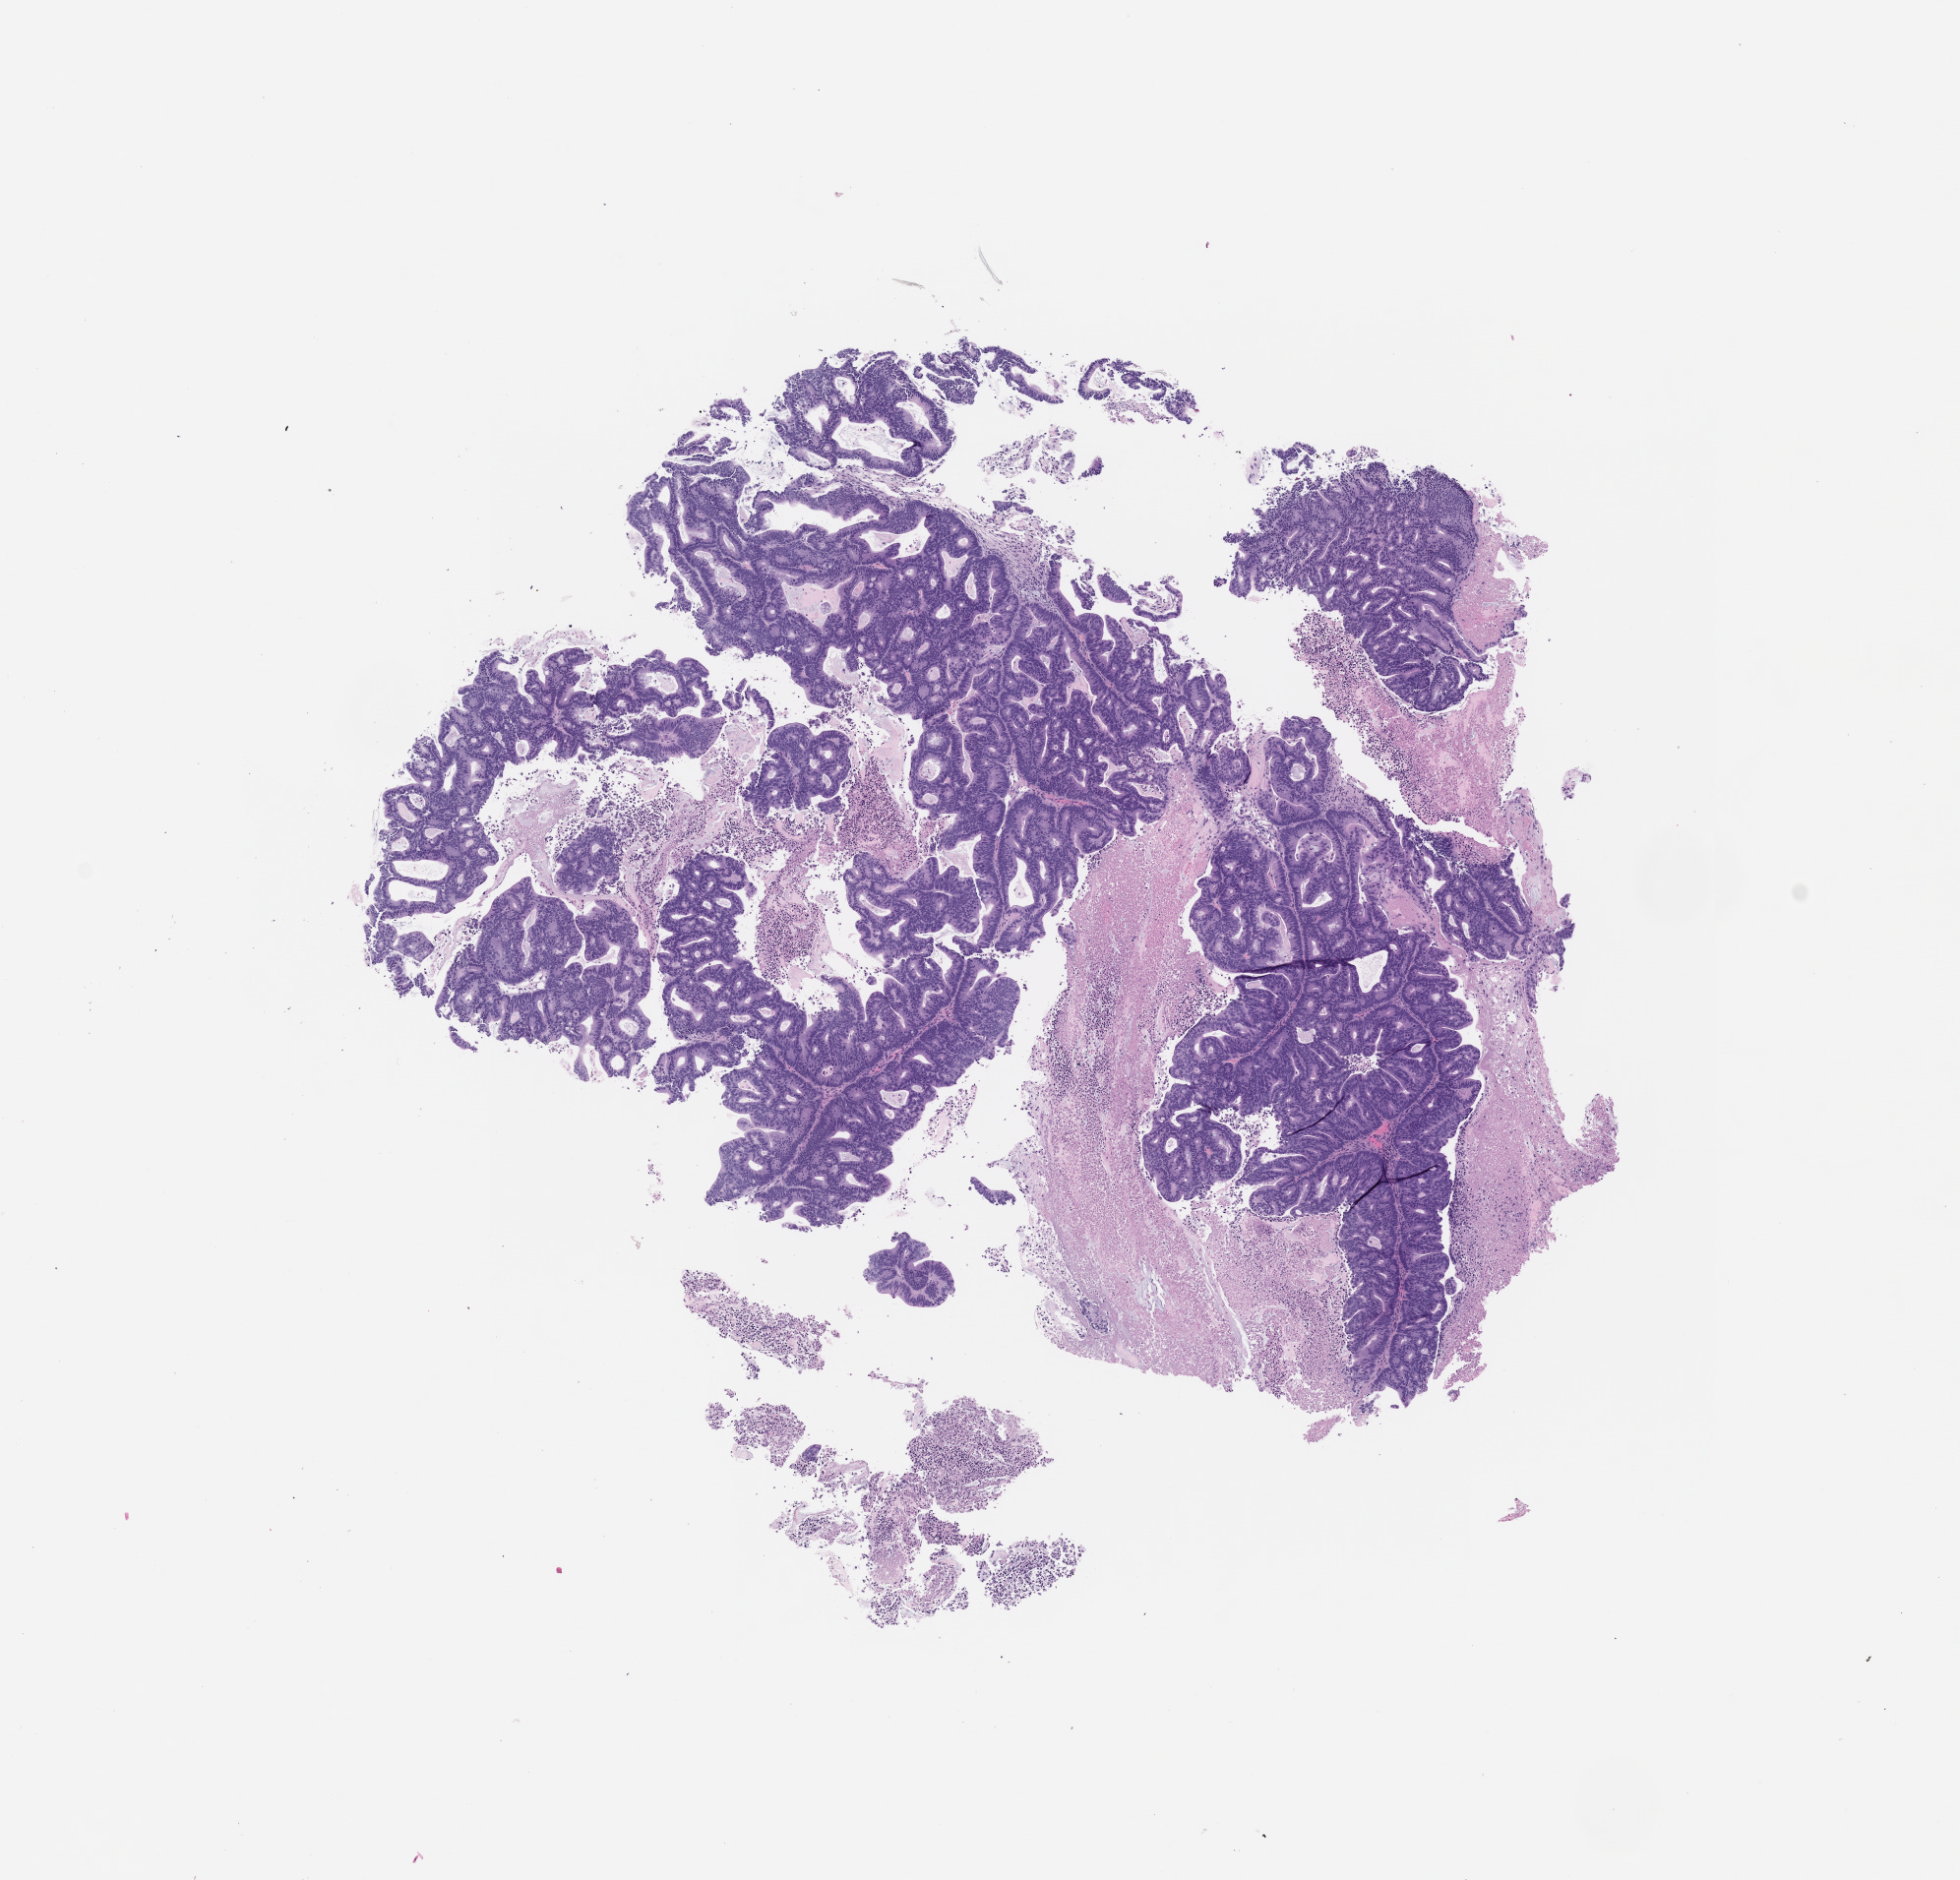
Whole-slide image, hematoxylin and eosin (H&E): patient-derived xenograft (human tumor grown in a mouse), passage 4, whole scanned area (about 8.0 x 7.7 mm) shown as a low-resolution overview; formalin-fixed paraffin-embedded section; originating tumor site category: colon.
Originating patient diagnosis: Colon Adenocarcinoma.